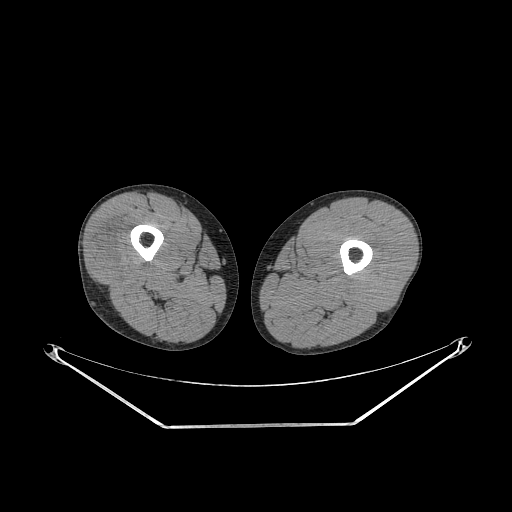
CT of an extremity soft-tissue mass (from a PET/CT study), one axial slice; position 225 of 267 along the scan axis; 140 kVp; soft-tissue window (W 400 / L 40 HU); 512 × 512 image matrix, field of view 500 × 500 mm. Male patient. From the clinical record (not read from this slice): histological type: poorly differentiated synovial sarcoma; grade: high; site of the primary tumour: right buttock.
Outlined on this slice (expert contour drawn on MRI and transferred to this co-registered scan by the dataset authors):
- gross tumour volume including surrounding oedema: bounding box (x1, y1, x2, y2) in pixels: (94, 233, 140, 277)